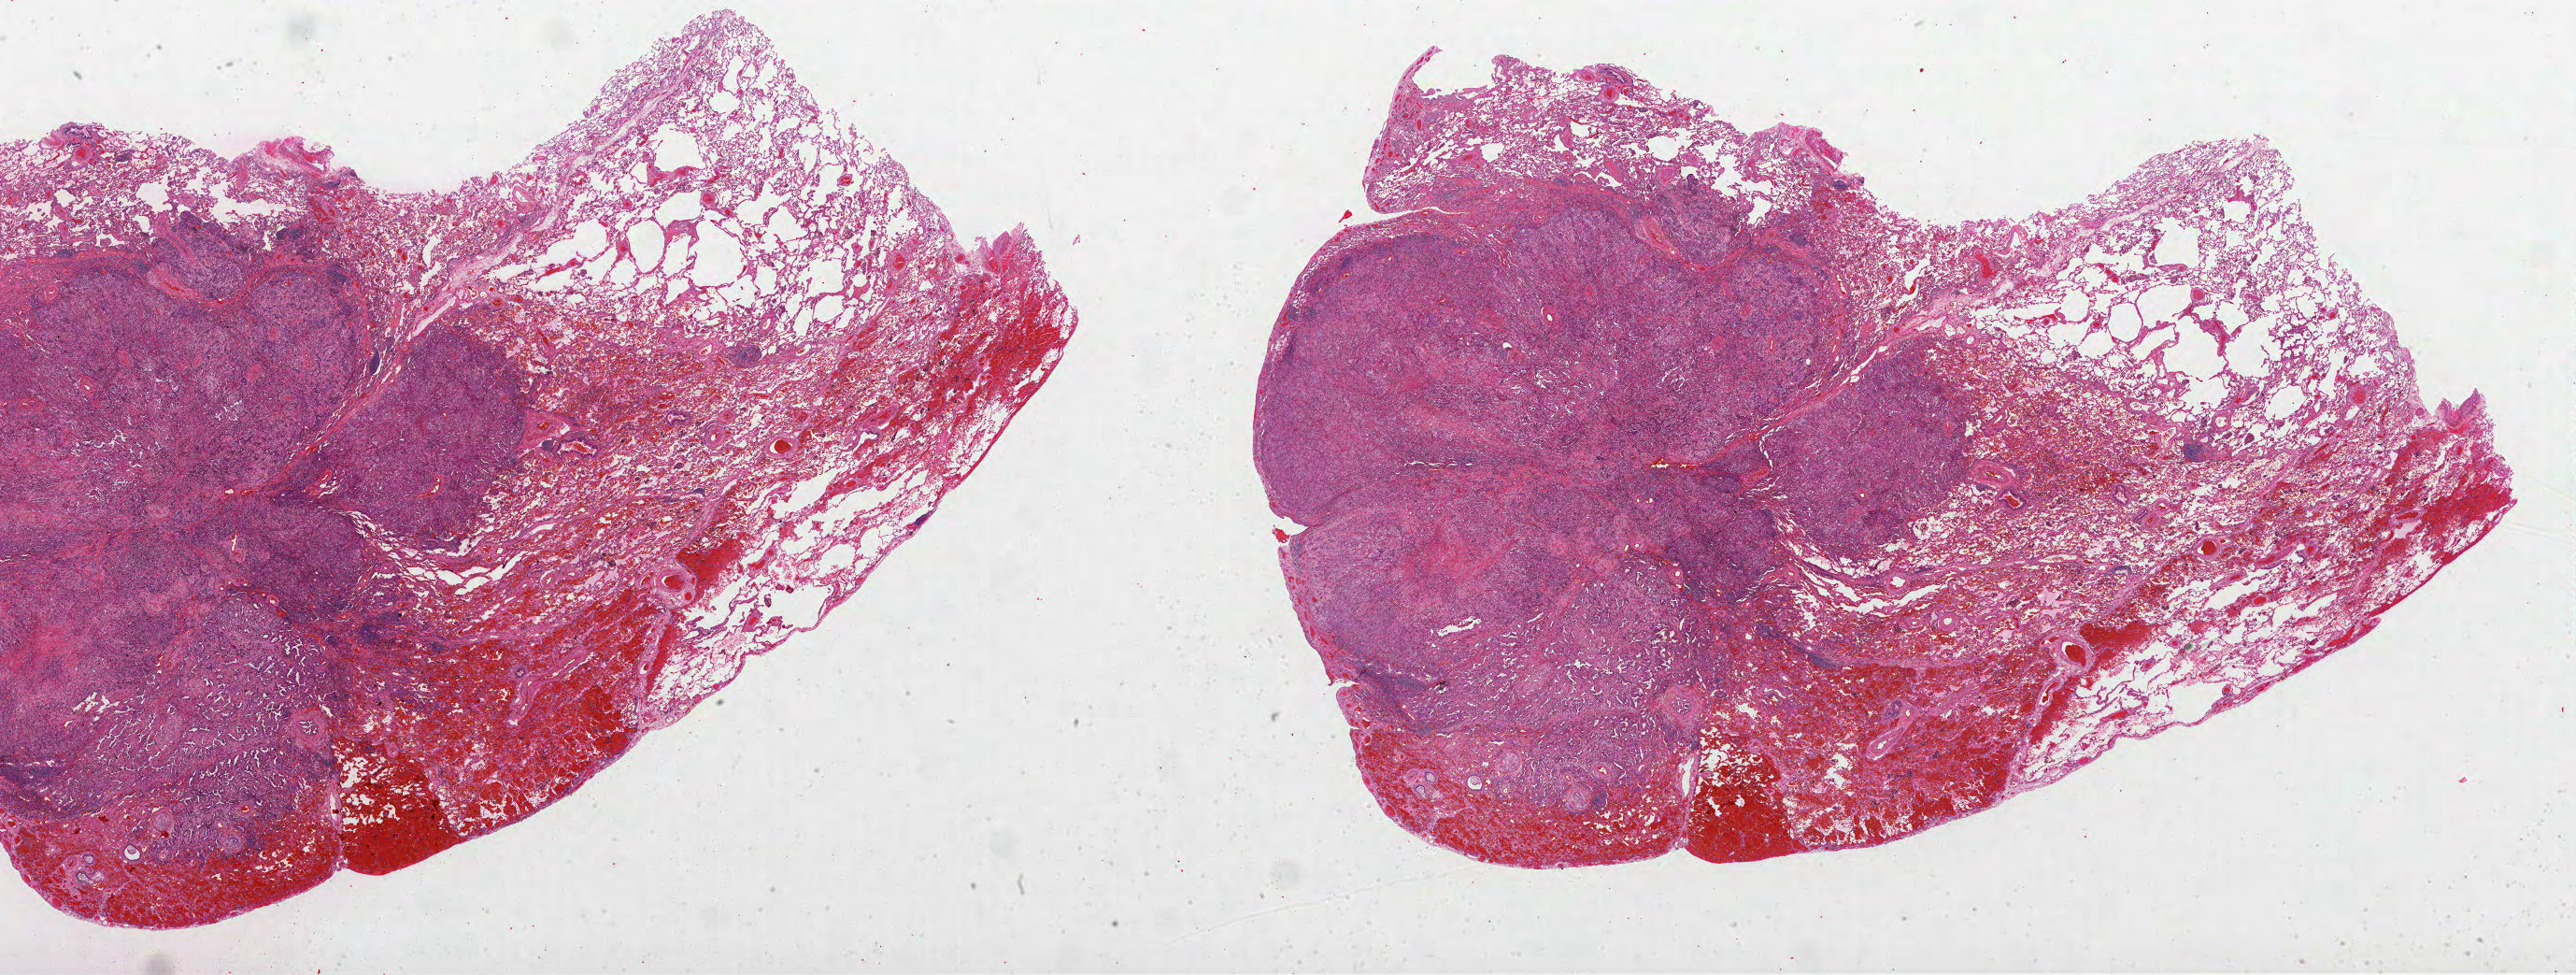
H&E-stained whole-slide image — shown as a low-resolution overview of the whole scanned area (about 44.5 x 16.8 mm). Formalin-fixed paraffin-embedded (FFPE) diagnostic section. Primary tumour sample from the lung. Female patient; age at initial diagnosis 68 years.
AJCC pathologic stage: IIIA. Histologic diagnosis: Adenocarcinoma, NOS (upper lobe, lung).